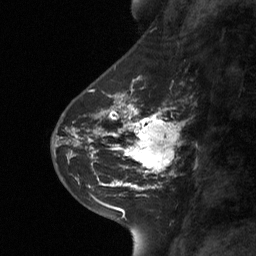
Breast MRI (dynamic contrast-enhanced), one sagittal slice; dynamic contrast-enhanced study with each time point stored as its own series, time point 2 of 3 at this slice position (early post-contrast, ordered by acquisition time); 1.5 T; TE 4.8 ms, TR 27 ms; 2 mm slice thickness; 256 × 256 image matrix, field of view 180 × 180 mm. Patient: female, 42 years. From the clinical record (not read from this slice): setting: breast cancer imaged before/during neoadjuvant chemotherapy; receptor status: triple-negative.
Annotated regions visible in this slice (semi-automatically segmented with operator editing):
- analysis volume of interest (the breast-tissue region the enhancement analysis was run in; not a lesion): box from (x=111, y=104) to (x=177, y=178) px
- tumour enhancement mask (voxels above the 90 % enhancement threshold inside the analysis volume of interest): (x=111, y=104)–(x=176, y=174)